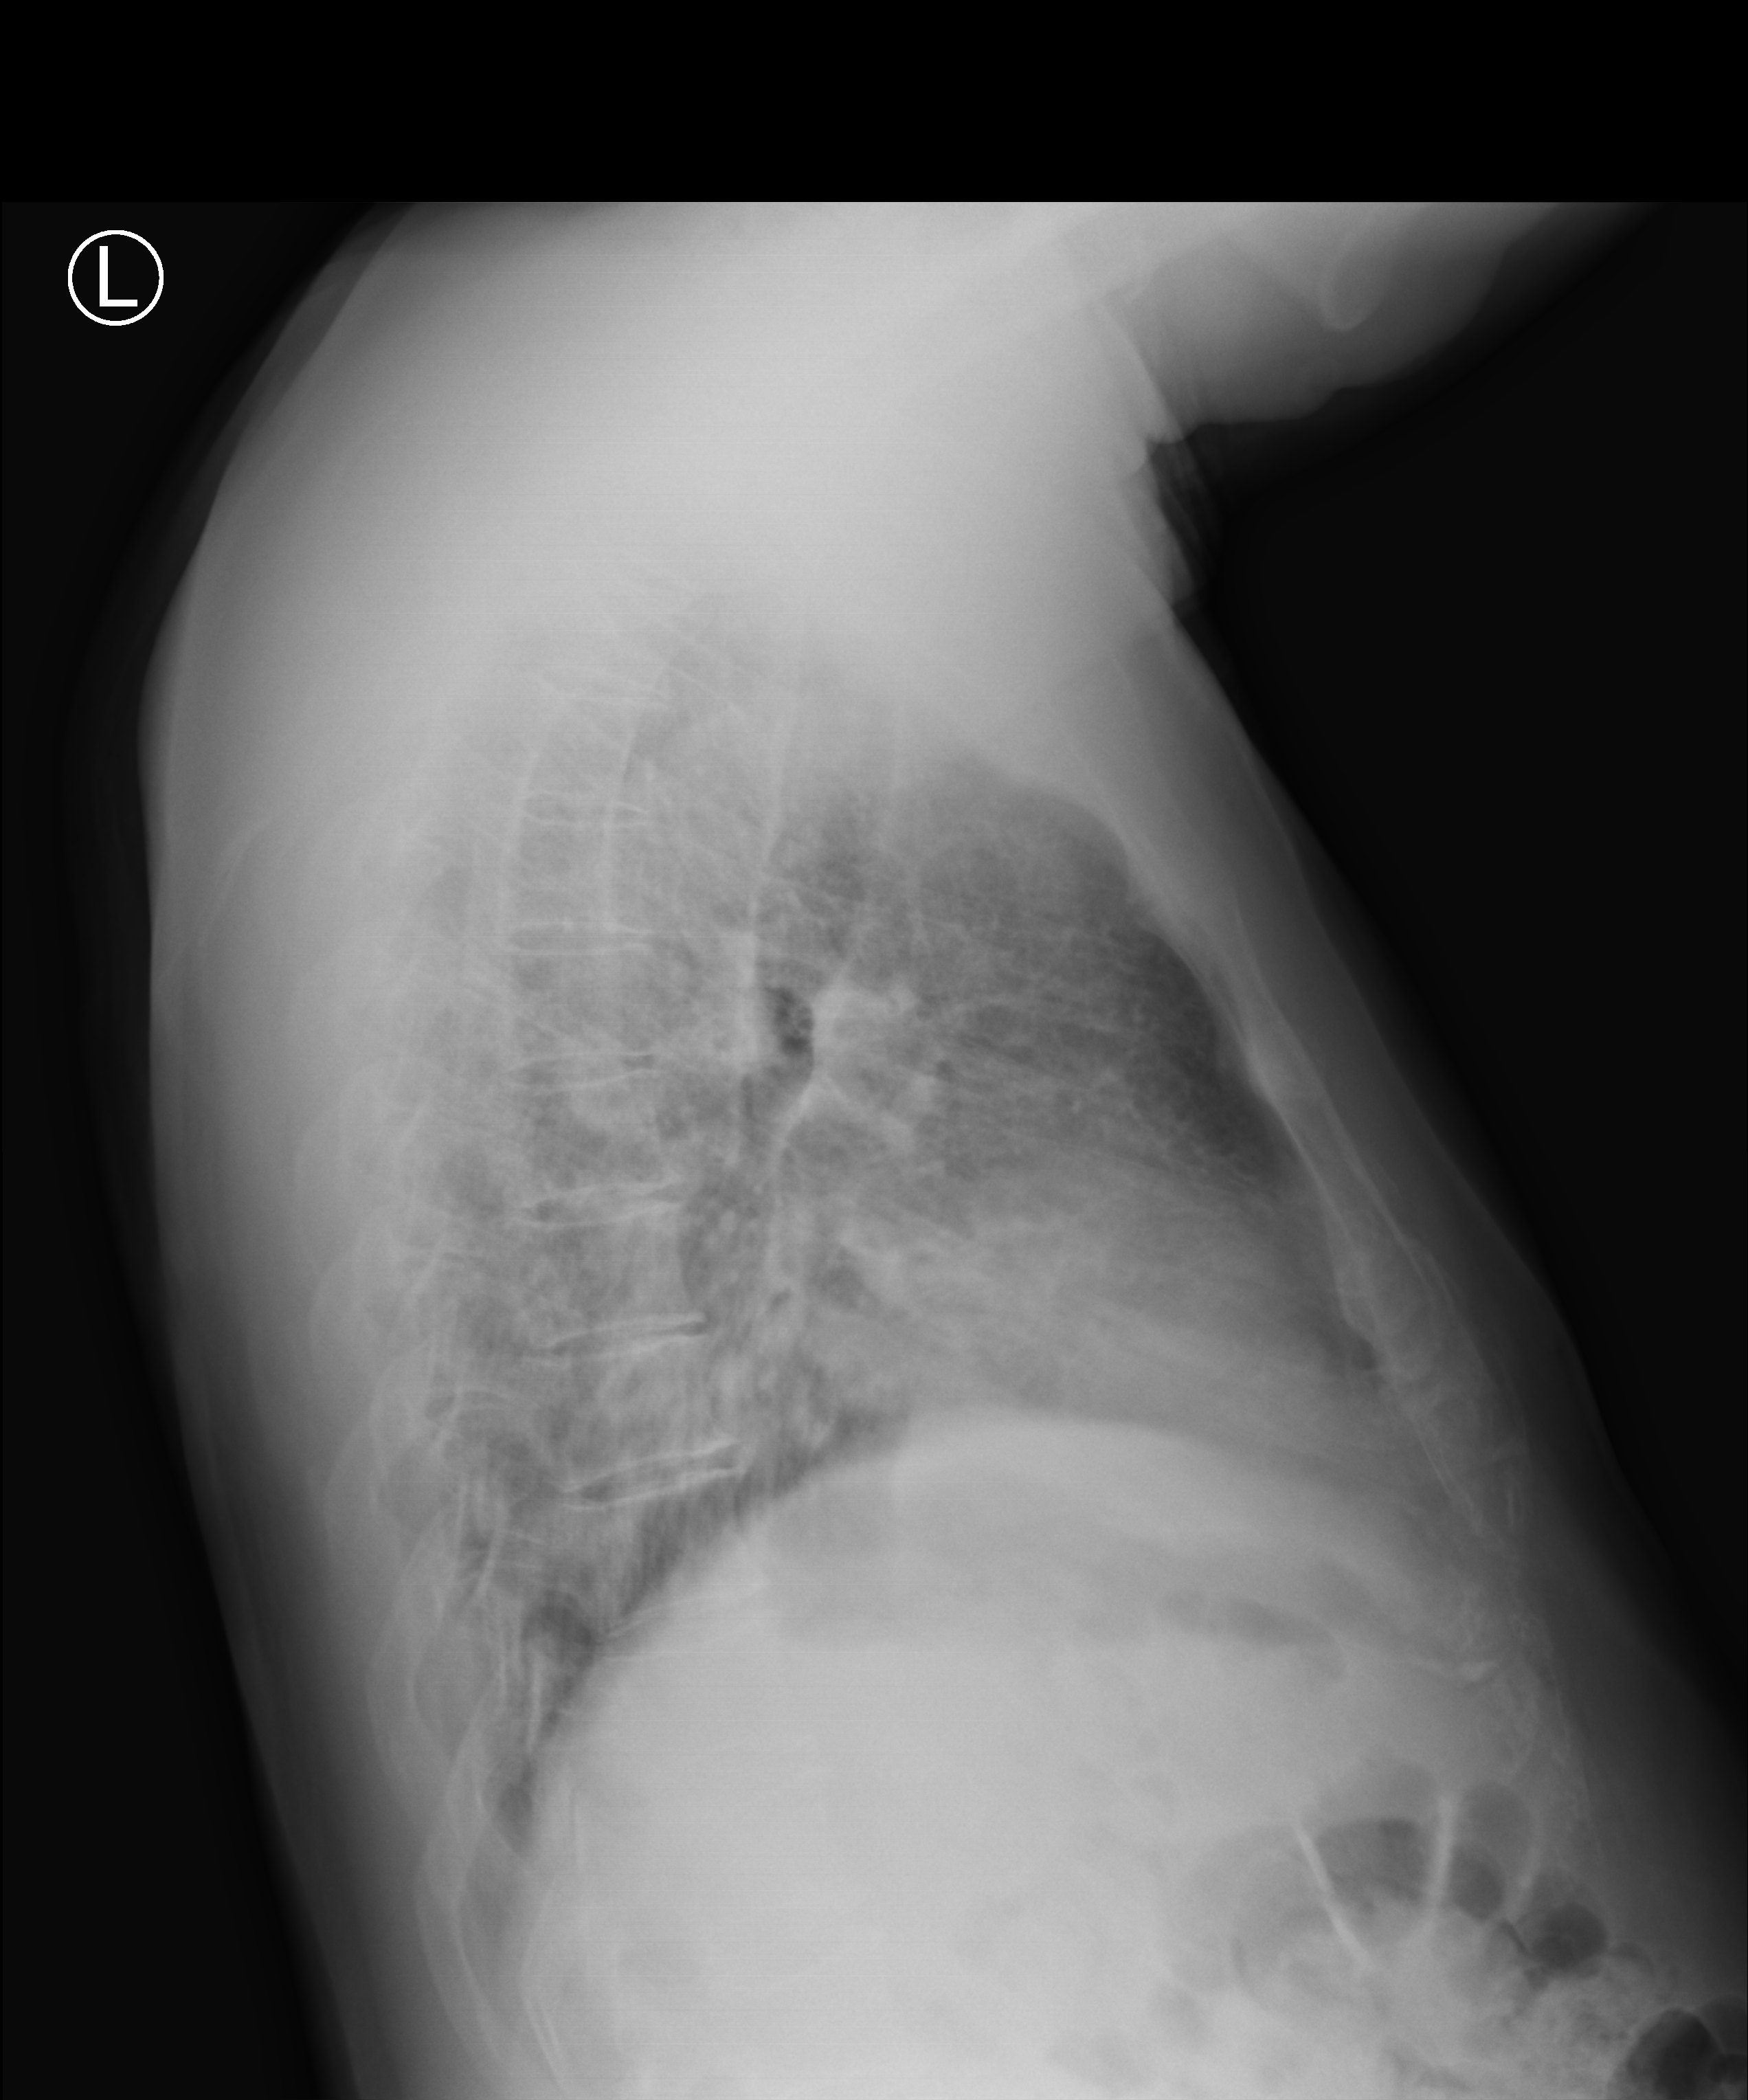
Chest X-ray; lateral projection. Patient hospitalised with COVID-19; male, aged 60–74 years.
From the hospital-stay record, not from the radiograph (when in the stay this image was taken is not recorded): admitted to intensive care during this hospital stay: no; mechanically ventilated during this hospital stay: no.